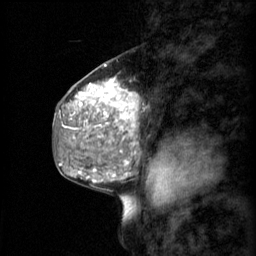
Breast MRI (dynamic contrast-enhanced), one sagittal slice; position 31 of 60 along the scan axis; 3 images stored at this slice position (order not interpretable as contrast timing); 1.5 T; TE 4.2 ms, TR 11 ms; 2 mm slice thickness; 256 × 256 image matrix, field of view 200 × 200 mm. Patient: female, 48 years.
Structures marked on this image (semi-automatically segmented with operator editing):
- analysis volume of interest (the breast-tissue region the enhancement analysis was run in; not a lesion): bounding box (x1, y1, x2, y2) in pixels: (69, 74, 140, 147)
- tumour enhancement mask (voxels above the 70 % enhancement threshold inside the analysis volume of interest): (74, 76, 138, 147)